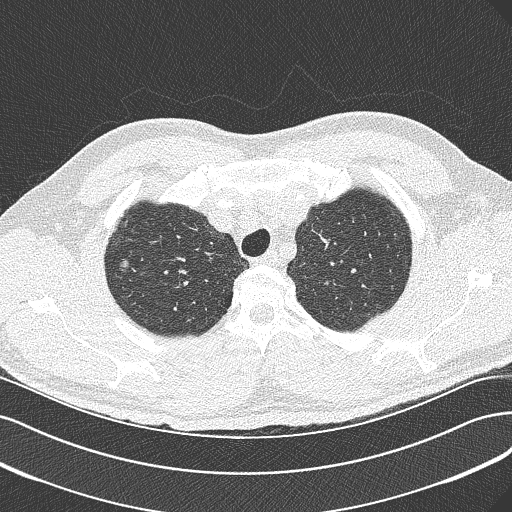
Axial slice from a low-dose chest CT screening exam; first (baseline) screen; lung window (W 1500 / L -600 HU); lung (sharp) reconstruction kernel (B50f); 120 kVp; slice 50 of 342 in the series; 512 × 512 image matrix. Male participant, aged 56 years at enrolment. Current smoker at enrolment.
- Expert-annotated lung lesion, box from (x=101, y=247) to (x=139, y=282) px.
- Screening reader's record for this exam (one nodule recorded; not confirmed to be the boxed lesion): non-calcified nodule or mass ≥4 mm, right upper lobe, 10 × 7 mm, spiculated (stellate) margins, soft tissue attenuation.
- Participant outcome: lung cancer diagnosed 517 days after this screen (after the second annual screen) — bronchiolo-alveolar carcinoma, non-mucinous, right upper lobe, moderately differentiated (G2), stage IIIB (AJCC 6th edition), 10 mm at pathology.